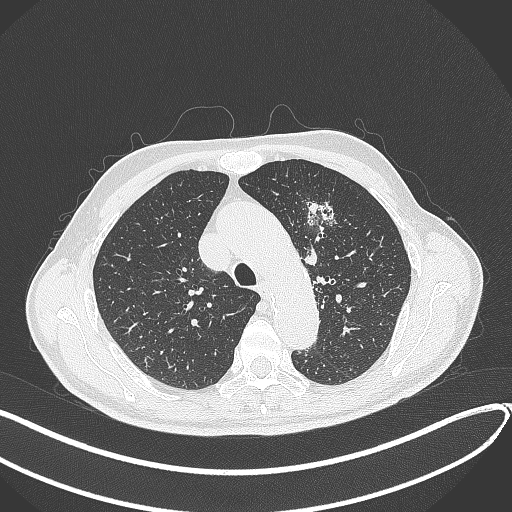
Chest CT, one axial slice; slice 303 of 459 in the series (ordered by position); 120 kVp; lung window (W 1500 / L -600 HU); 1 mm slice thickness; 512 × 512 image matrix, field of view 400 × 400 mm. Male patient, age 74 years. Case-level facts recorded for this patient, not image findings: clinical TNM (as recorded): T2b N0 M1c.
Outlined on this slice (rectangle marked by the reading radiologist):
- lung tumour (recorded histology: adenocarcinoma): bounding box (x1, y1, x2, y2) in pixels: (301, 195, 345, 246)